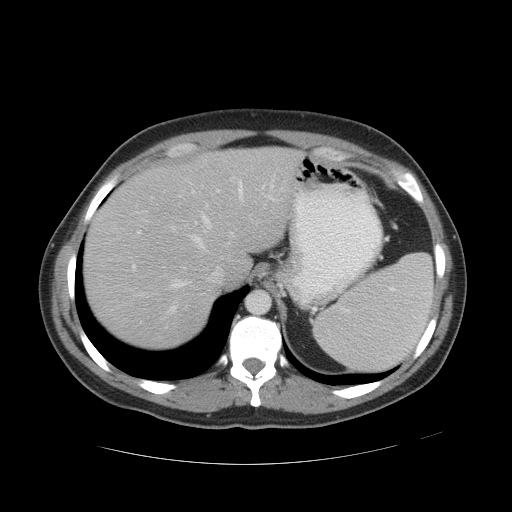
Contrast-enhanced abdominal CT, one axial slice. Position 39 of 49 along the scan axis. 120 kVp. Intravenous contrast given. Soft-tissue window (W 400 / L 40 HU). 5 mm slice thickness. 512 × 512 image matrix, field of view 422 × 422 mm. Male patient, age 42 years. From the clinical record (not read from this slice): diagnosis: colorectal cancer liver metastases, imaged before liver resection; multiple liver metastases: yes; largest metastasis: 2.8 cm; disease in both lobes: yes.
Structures marked on this image (manually delineated by an expert):
- hepatic veins: box from (x=128, y=173) to (x=266, y=317) px
- liver: (x=84, y=149)–(x=296, y=348)
- planned liver remnant (the part of the liver to remain after resection): (x=84, y=148)–(x=297, y=348)
- portal vein (with intrahepatic branches): (x=132, y=178)–(x=265, y=271)